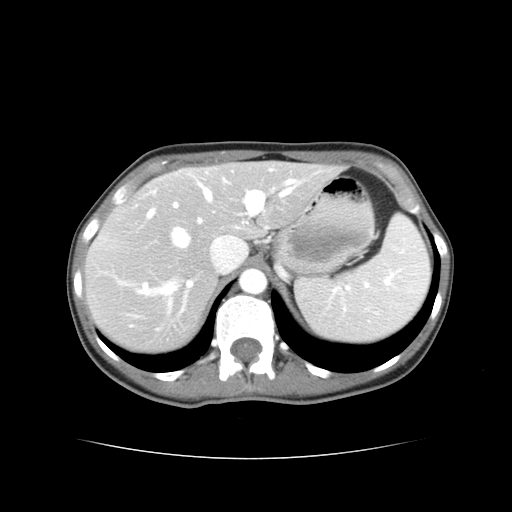
Contrast-enhanced abdominal CT, one axial slice. Slice 28 of 38 in the series (ordered by position). Reconstruction kernel STANDARD. 120 kVp. Intravenous contrast given. Soft-tissue window (W 400 / L 40 HU). 5 mm slice thickness. 512 × 512 image matrix, field of view 340 × 340 mm. Female patient, age 54 years. From the clinical record (not read from this slice): diagnosis: colorectal cancer liver metastases, imaged before liver resection; multiple liver metastases: yes; largest metastasis: 1.1 cm; disease in both lobes: yes.
Annotated regions visible in this slice (manually delineated by an expert):
- hepatic veins: bounding box (x1, y1, x2, y2) in pixels: (158, 189, 291, 294)
- liver: (86, 164, 336, 351)
- planned liver remnant (the part of the liver to remain after resection): (210, 164, 336, 236)
- portal vein (with intrahepatic branches): (140, 180, 296, 295)